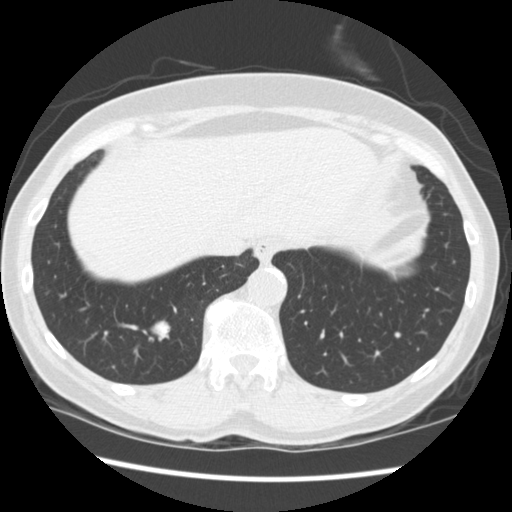
Low-dose screening chest CT, one axial slice. Position 59 of 262 along the scan axis. Reconstruction kernel STANDARD. Lung window (W 1500 / L -600 HU). 2.5 mm slice thickness. 512 × 512 image matrix.
Outlined on this slice (outlined manually by an expert reader):
- lesion 1 (tumor, lower lobe of right lung): bounding box <150,321,170,340> (left, top, right, bottom; pixels)